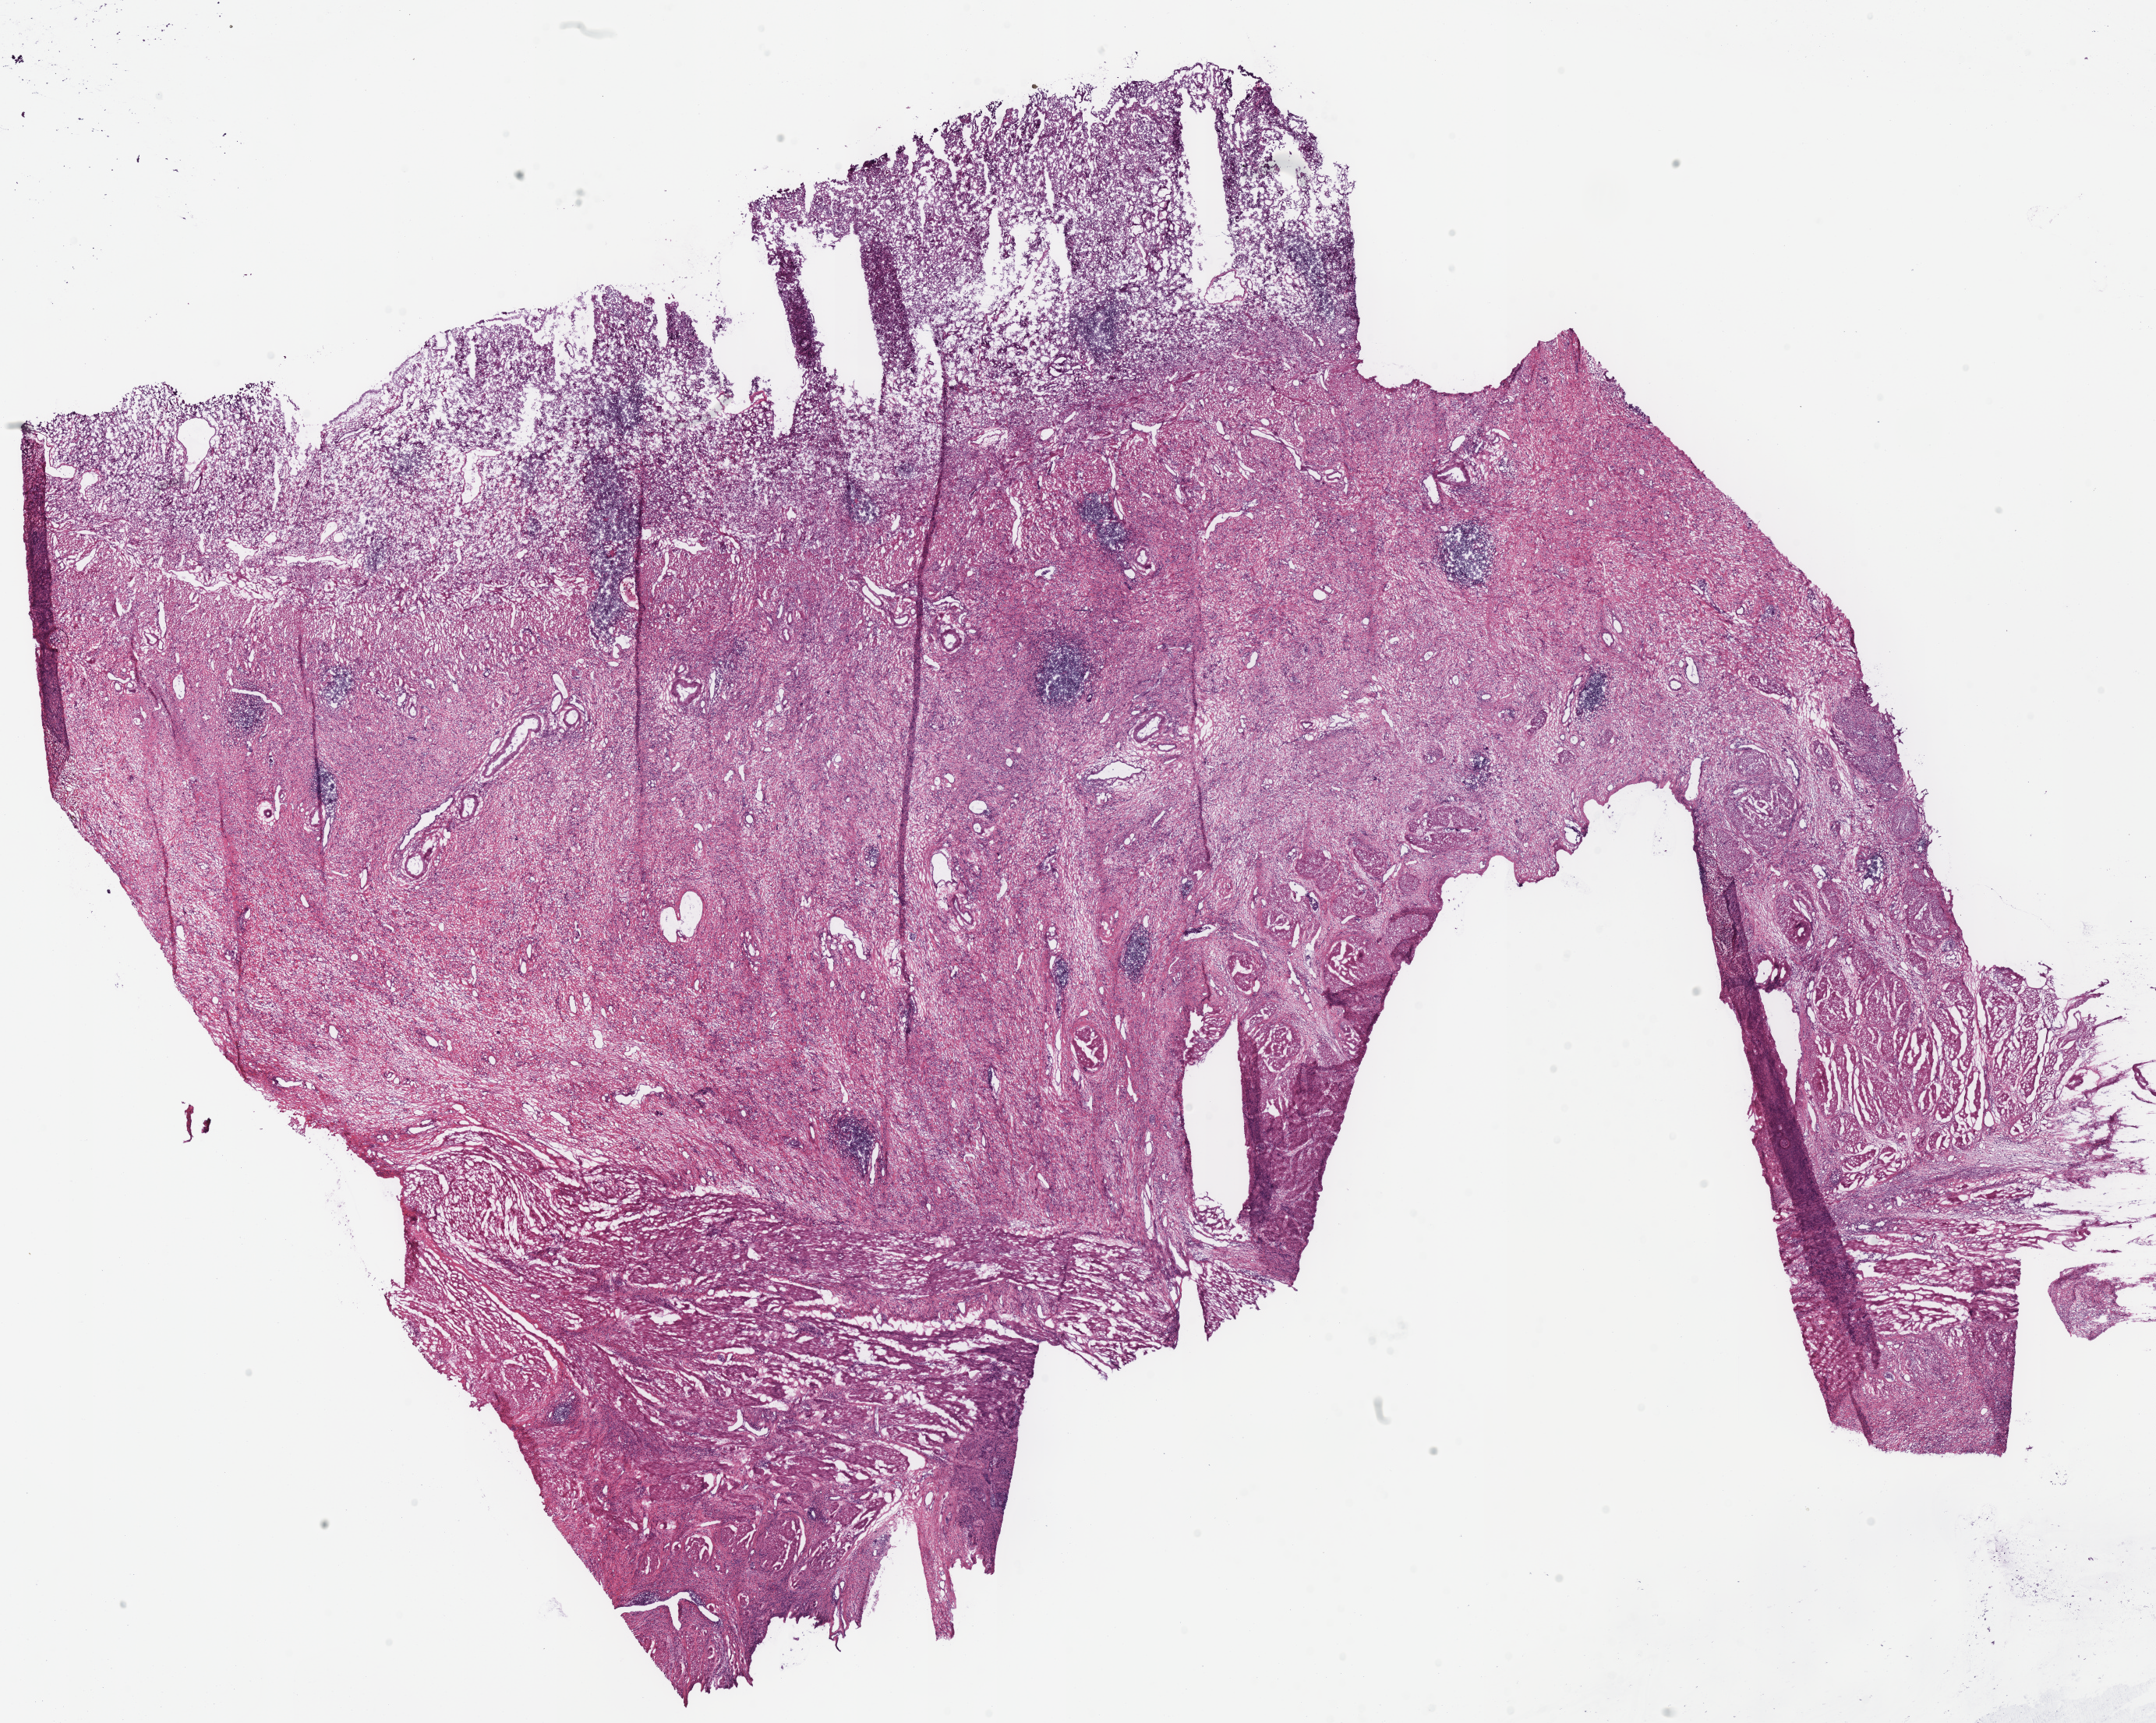
Whole-slide histology image, H&E — whole scanned area (about 21.8 x 17.4 mm, from a 40x scan) shown as a low-resolution overview; frozen section from the bottom of the tissue portion; stomach, primary tumour sample. Male patient; age at initial diagnosis 62 years. Pathologist review of this section (percent, as recorded): tumour cells 65%, tumour nuclei 50%.
Diagnosis: Adenocarcinoma, NOS (cardia, NOS).